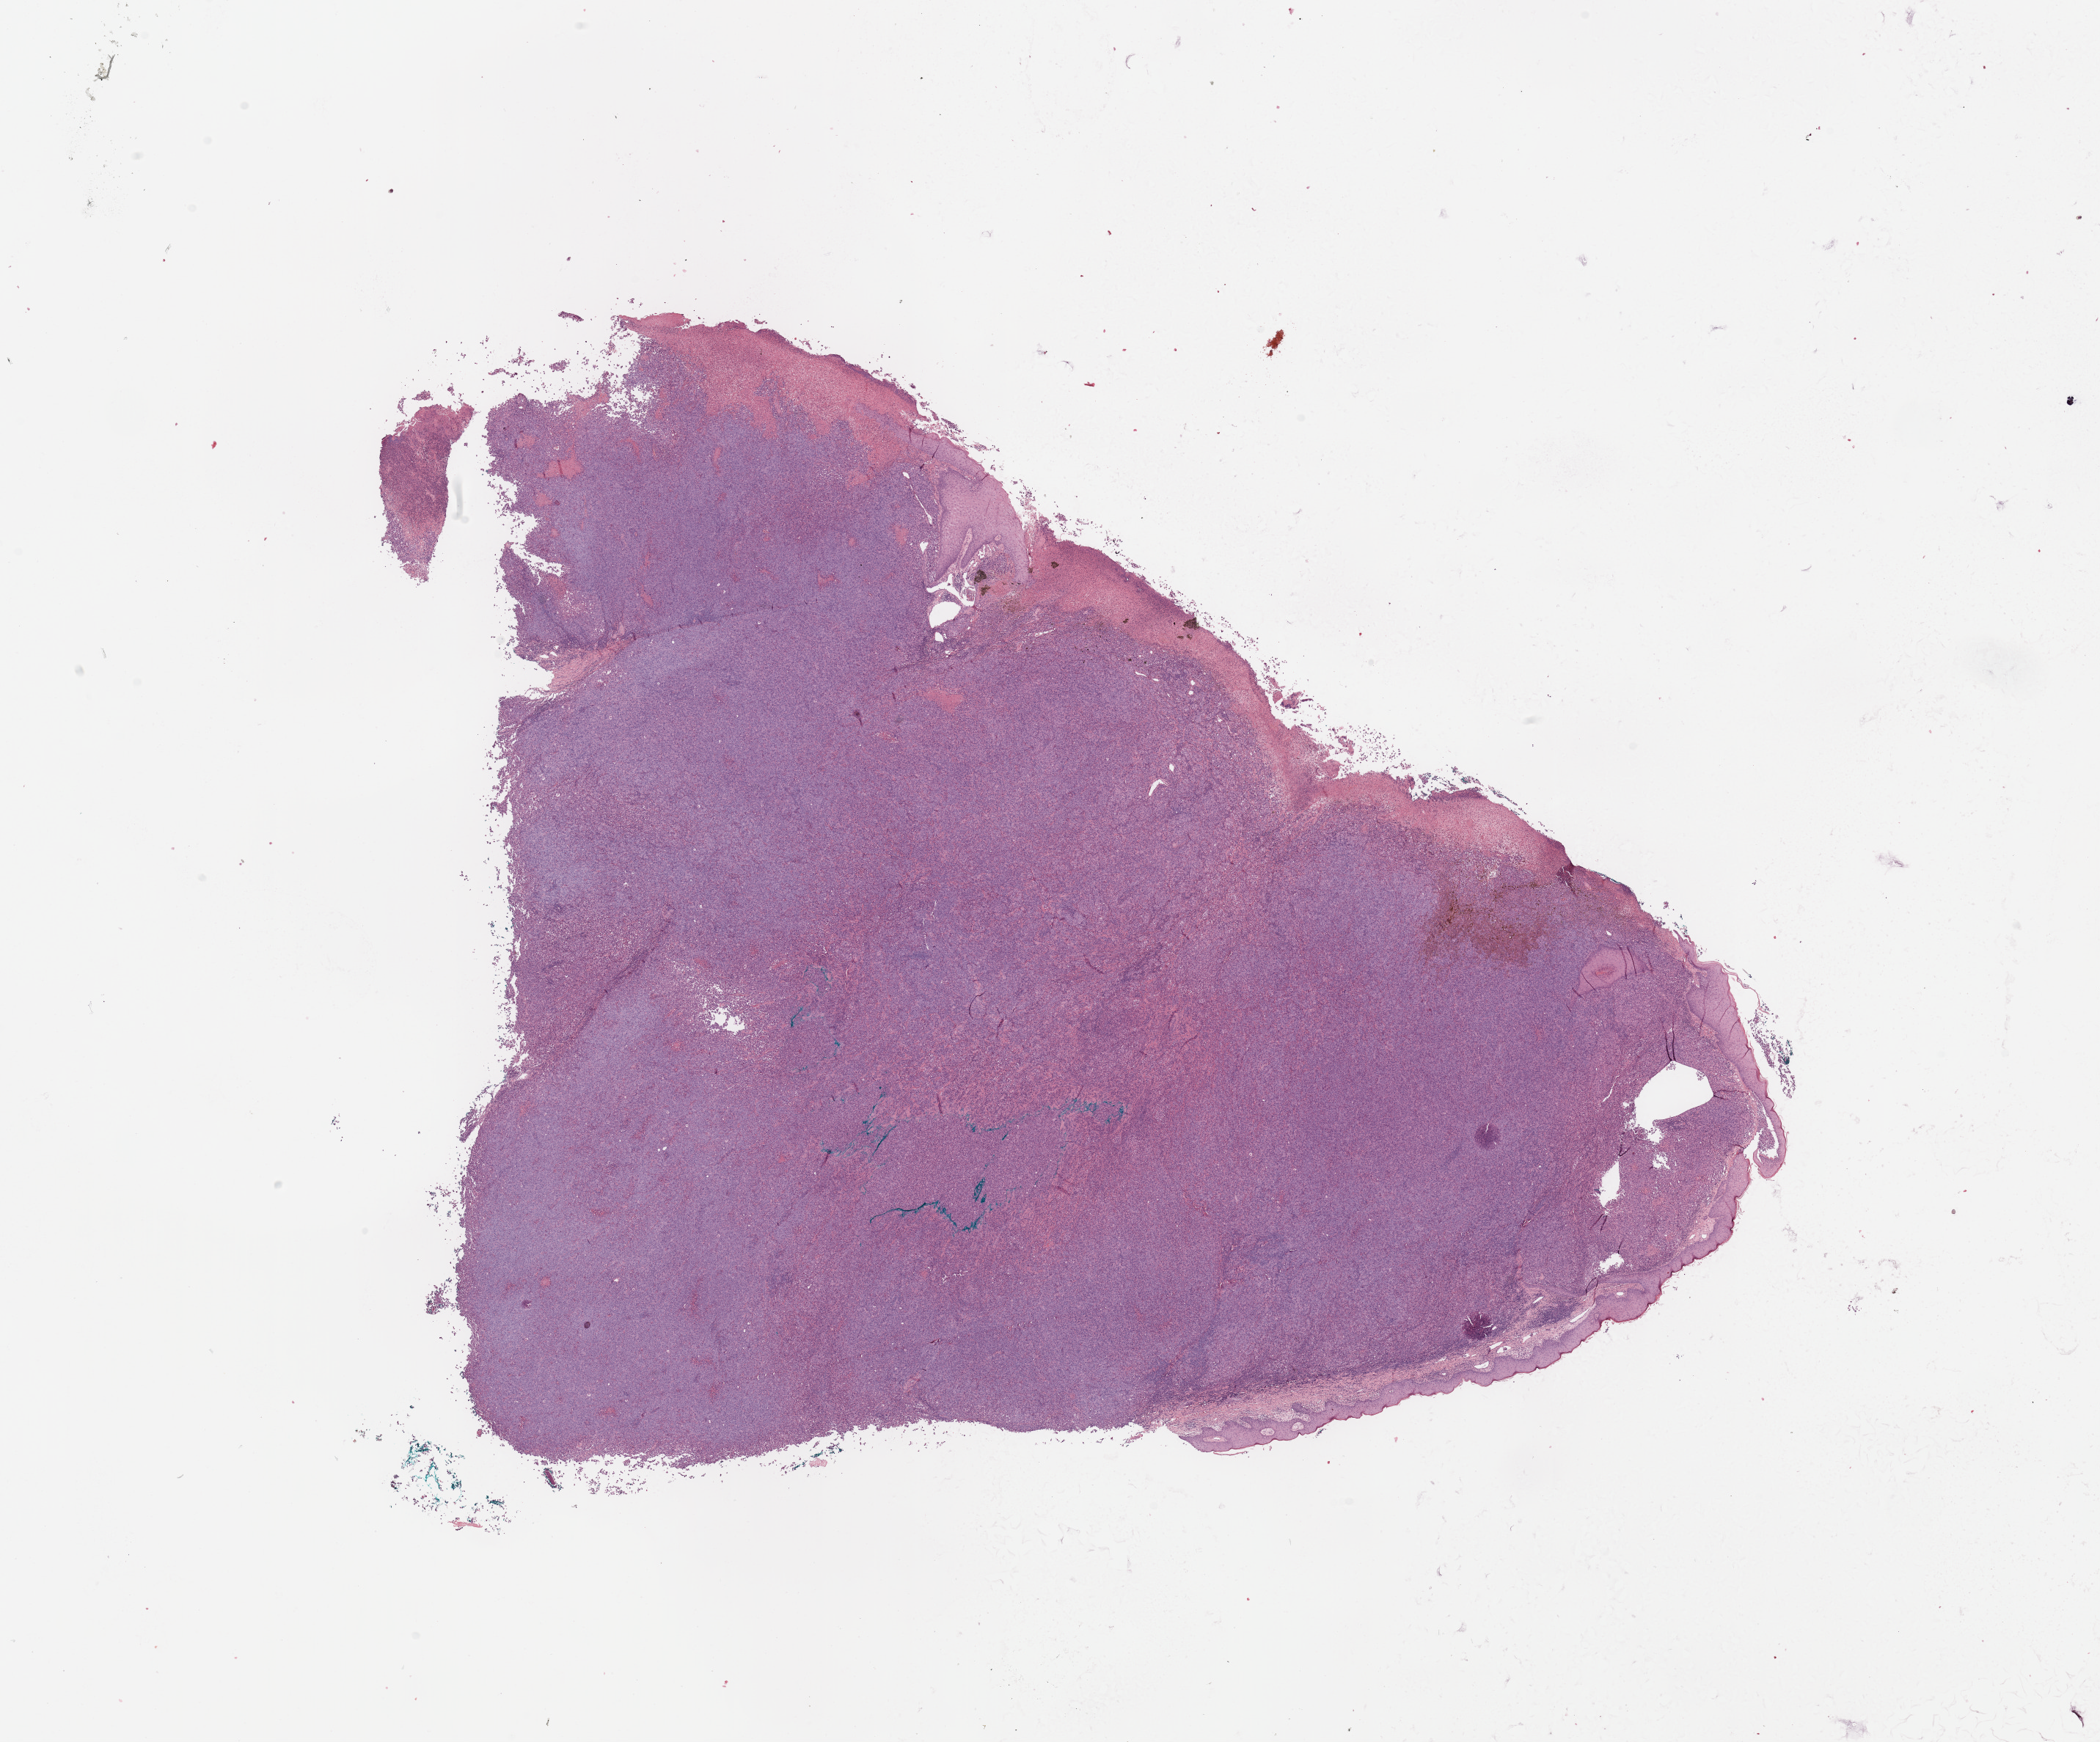
Digitized Hematoxylin and eosin (H&E) stained tissue section (whole slide), whole scanned area (about 22.6 x 18.8 mm) shown as a low-resolution overview. Tumour tissue sample, sampled site: trunk. Male, 57 y/o. Slide review estimates, as recorded: tumour nuclei 90%, necrosis 5%.
Histologic diagnosis: Malignant melanoma, NOS. AJCC pathologic stage: IIC. Primary tumour site (as recorded): trunk.